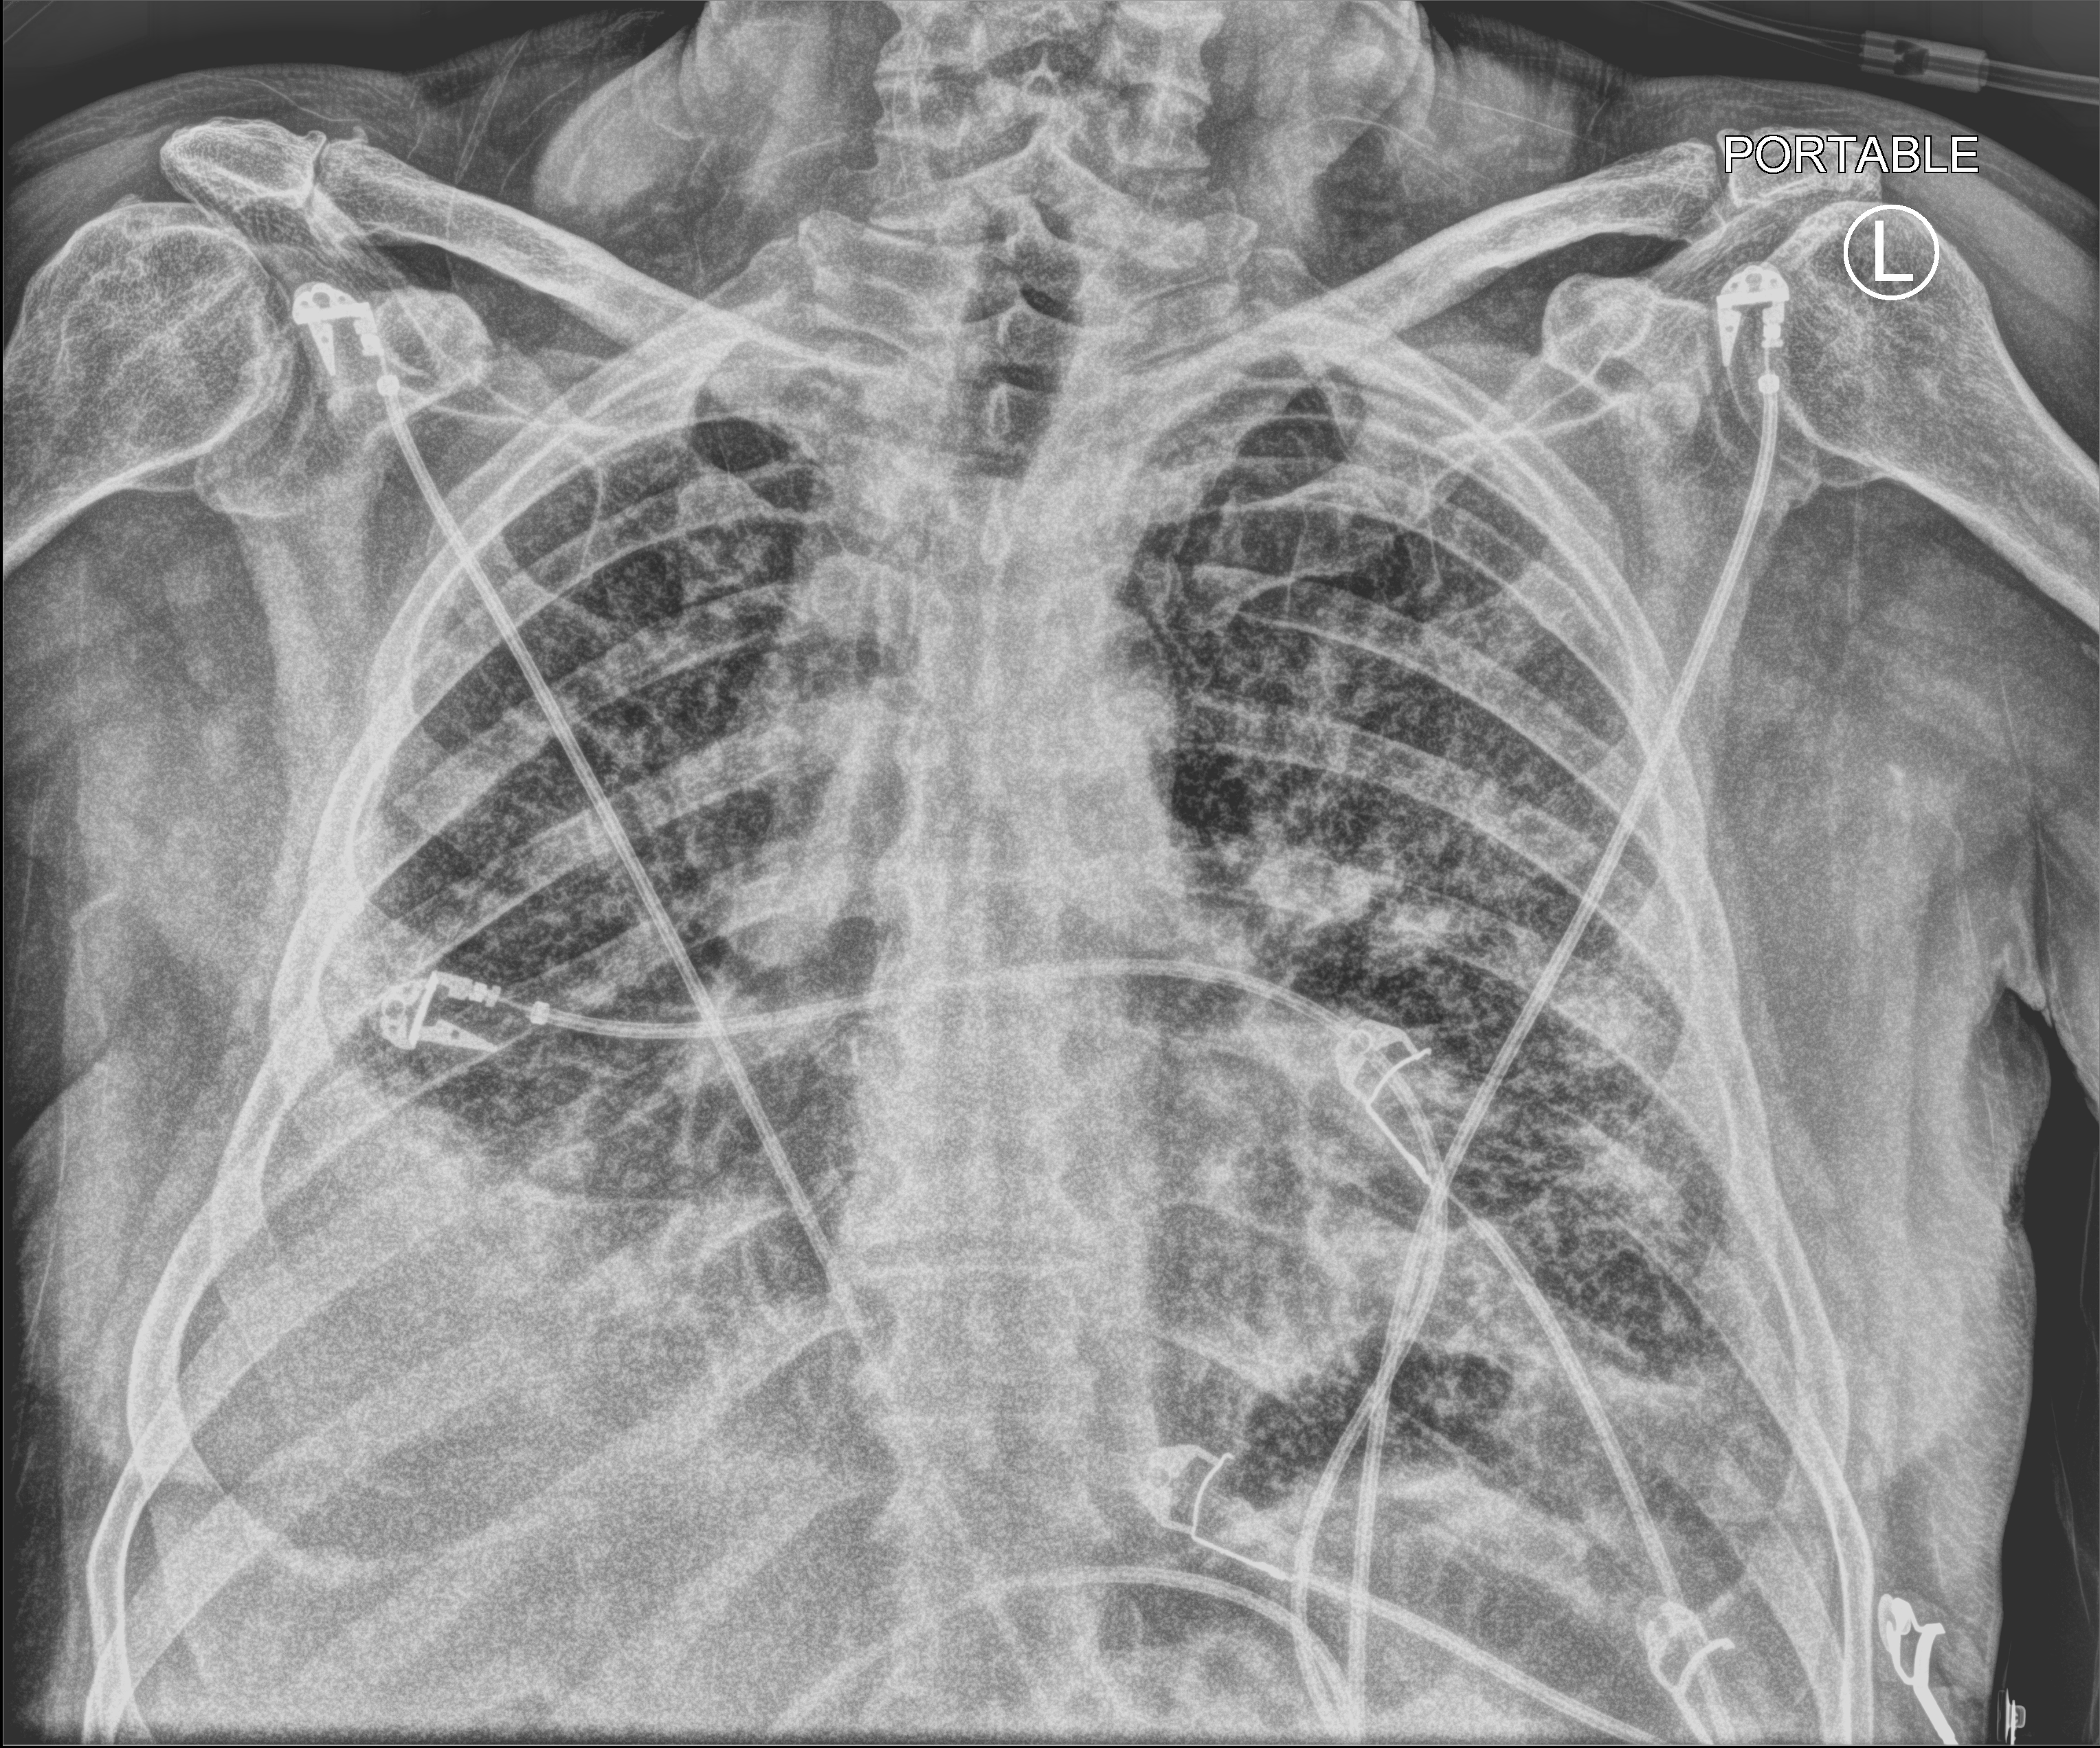
Portable chest radiograph; anteroposterior (AP) projection. Male patient hospitalised with COVID-19, age 75–90 years.
Admission-level facts for this patient (not findings on this image; timing relative to this image not recorded):
- mechanically ventilated during this hospital stay: no